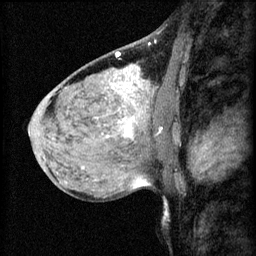
Breast MRI (dynamic contrast-enhanced), one sagittal slice. Slice 39 of 60 in the series (ordered by position). 3 images stored at this slice position (order not interpretable as contrast timing). 1.5 T. TE 4.2 ms, TR 8.2 ms. 256 × 256 image matrix, field of view 180 × 180 mm. Female patient, age 40 years.
Annotated regions visible in this slice (semi-automatic segmentation, software-assisted and operator-edited):
- analysis volume of interest (the breast-tissue region the enhancement analysis was run in; not a lesion): bounding box [x1, y1, x2, y2] px = [108, 82, 175, 139]
- tumour enhancement mask (voxels above the 70 % enhancement threshold inside the analysis volume of interest): [112, 82, 163, 137]